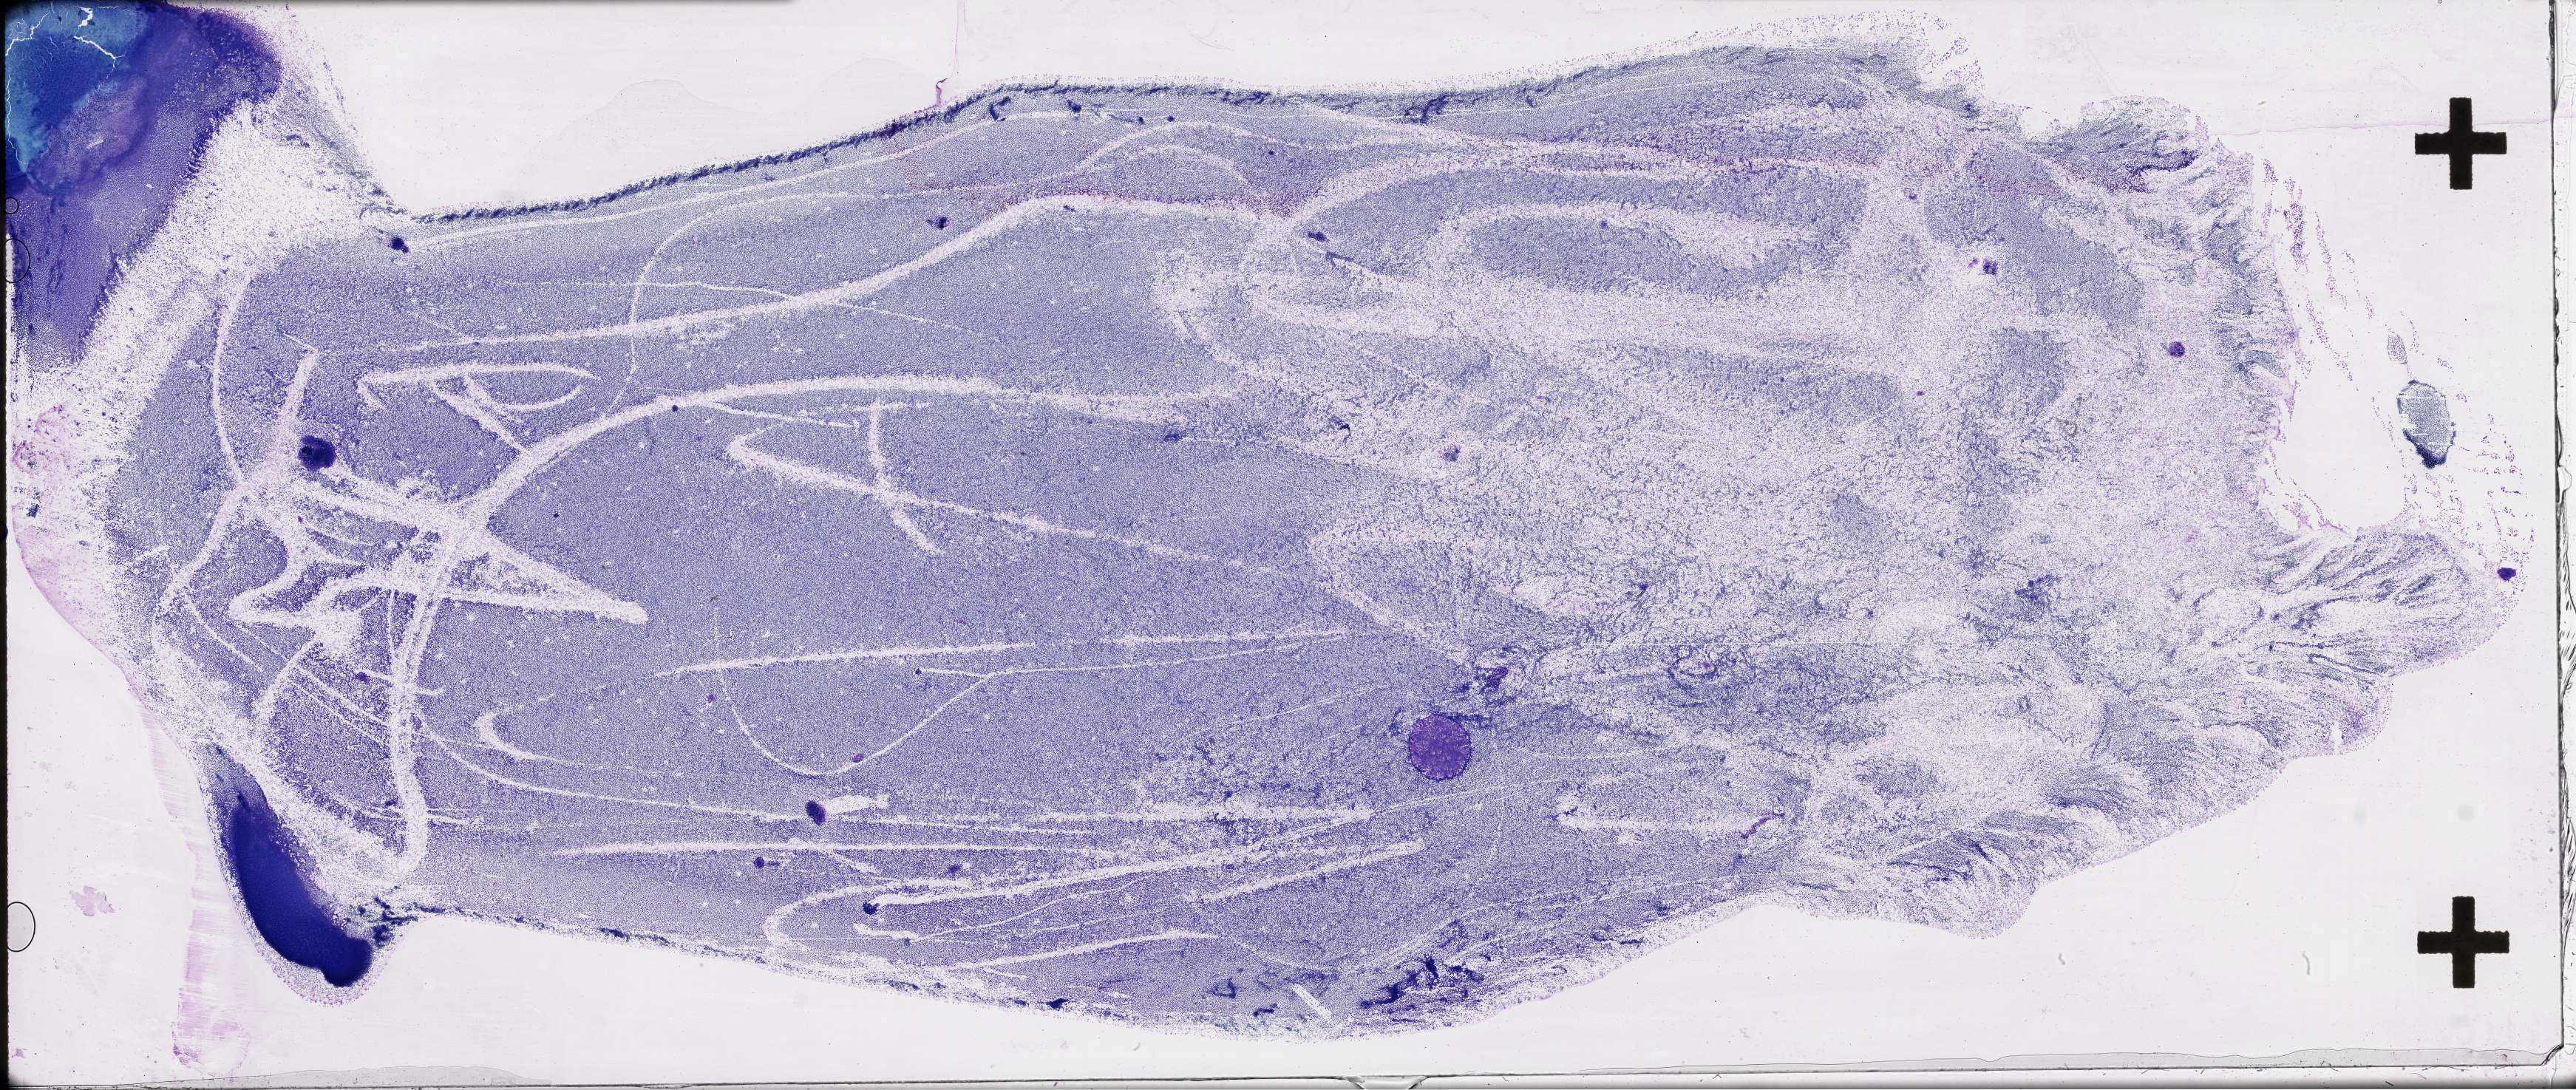
Whole-slide histology image, H&E-stained, a low-resolution overview of the entire scanned area, about 56.3 x 23.8 mm (slide scanned at 40x). Bone marrow (leukaemic) sample. Blasts: 90%.
FAB classification: M4. Diagnosis: Acute Myeloid Leukemia.